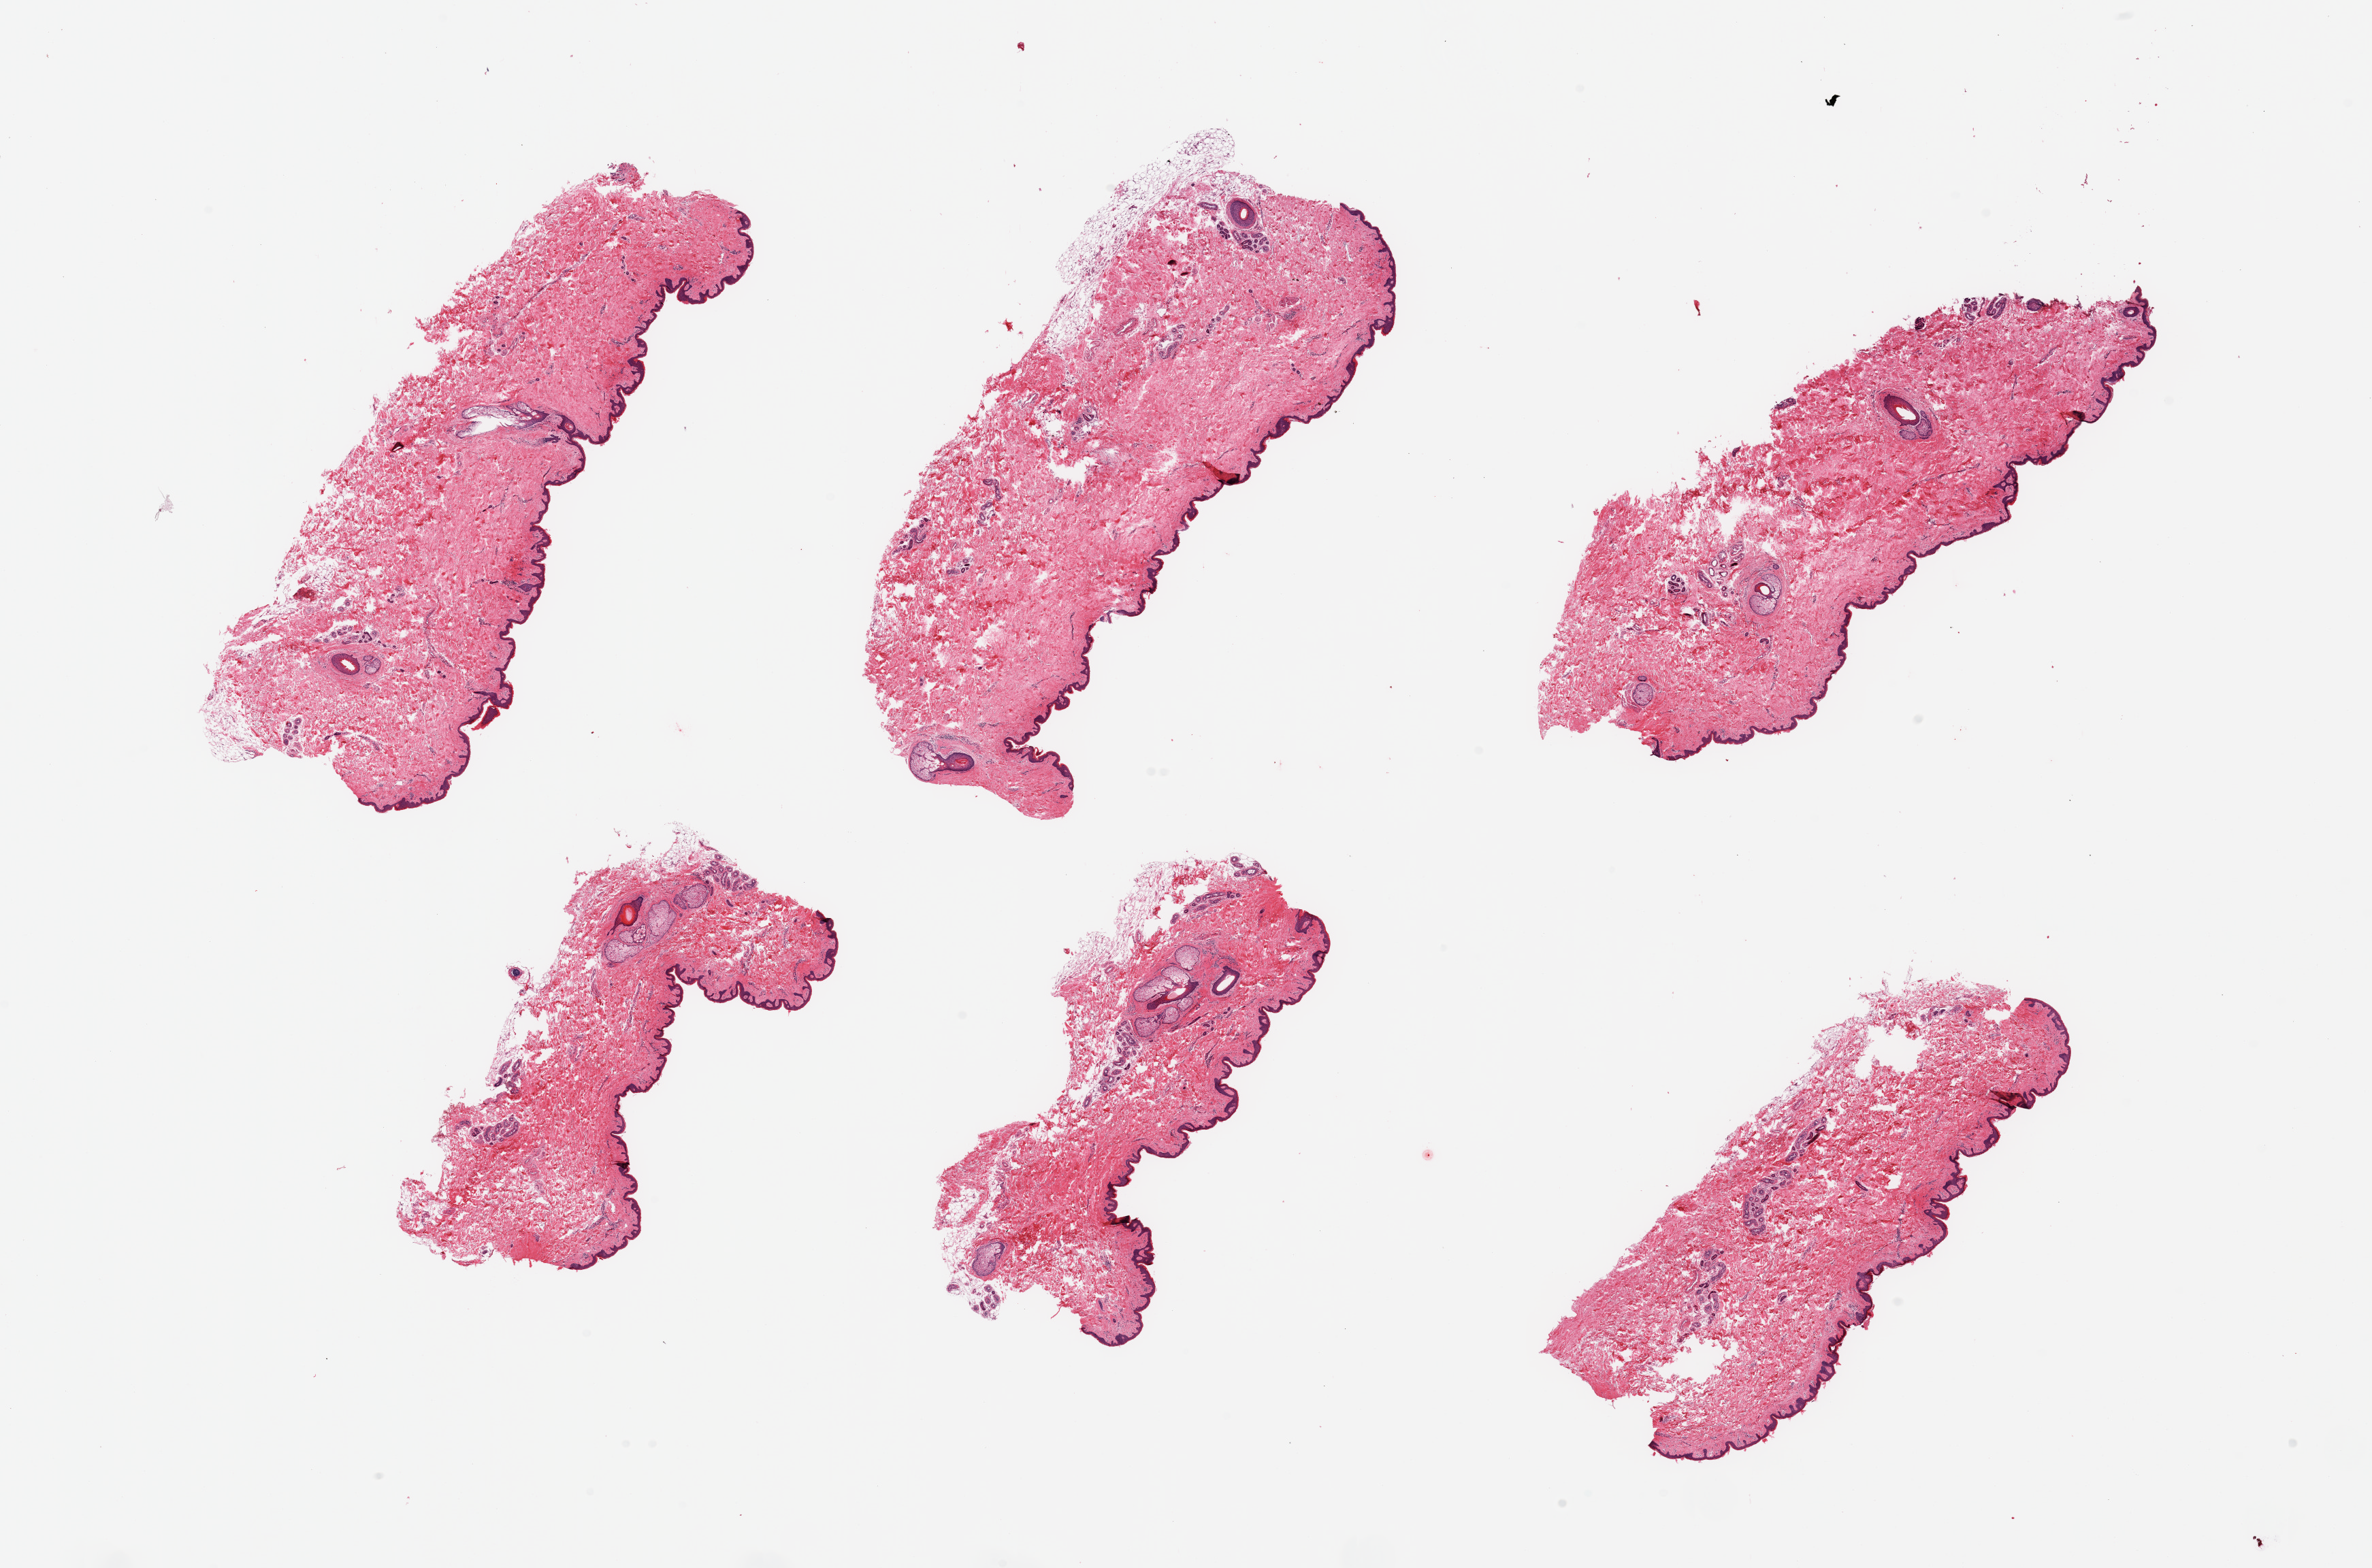
Haematoxylin and eosin whole-slide image, brightfield, low-resolution overview of the scanned area, about 27.6 x 18.2 mm, PAXgene-fixed, paraffin-embedded tissue, section of skin of suprapubic region (target tissue), tissue donor sample. Donor sex: male.
Reviewer comment on this tissue sample: 6 pieces, no dermal fat, squamous epithelium is ~30-40 microns.